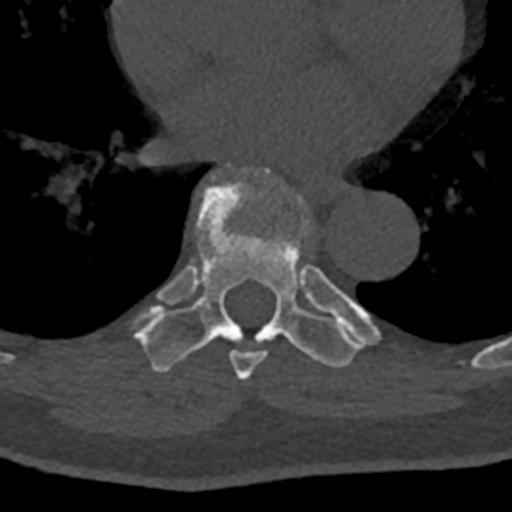
CT including the spine, one axial slice; position 727 of 797 along the scan axis; 120 kVp; bone window (W 1800 / L 400 HU); 0.5 mm slice thickness; 512 × 512 image matrix. Male patient, age 74 years. Case-level facts recorded for this patient, not image findings: primary cancer: renal; vertebrae with lytic lesions (as recorded): T10, L1, L2, L3, L4, L5.
Outlined on this slice (semi-automatic segmentation, software-assisted and operator-edited):
- T7 vertebra: bounding box (x1, y1, x2, y2) in pixels: (223, 167, 351, 380)
- T8 vertebra: (134, 163, 380, 372)